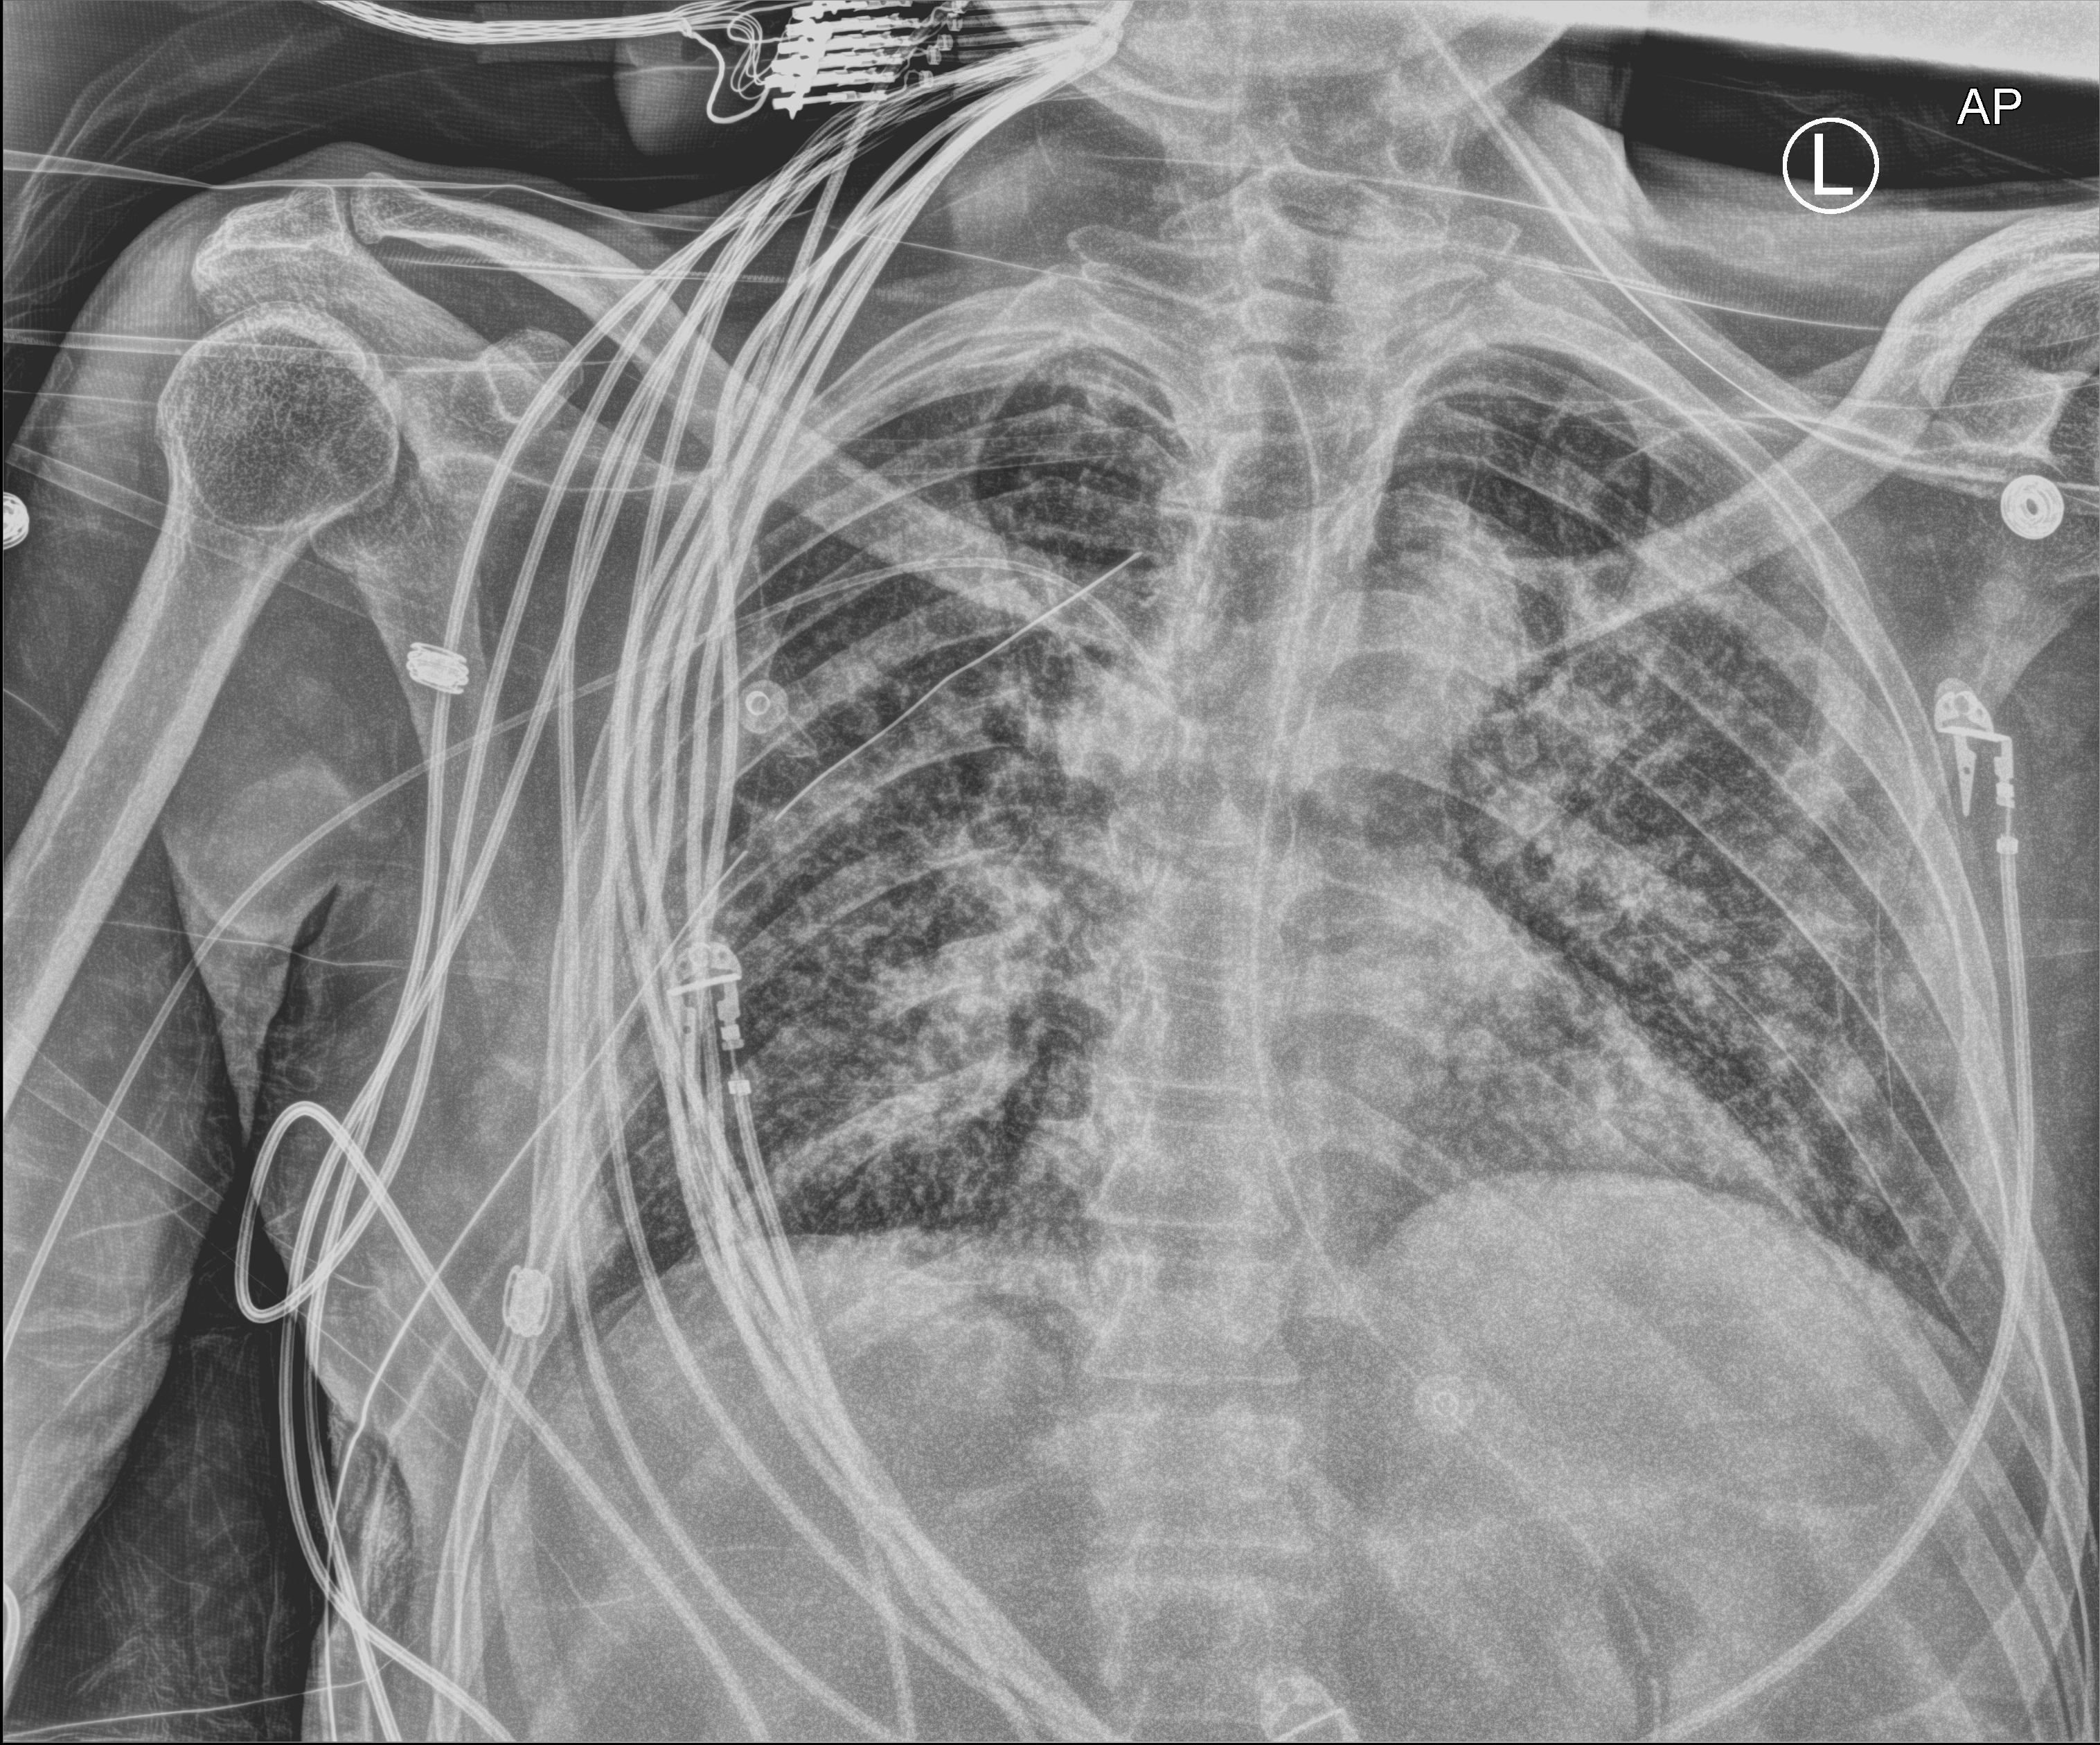
Bedside chest radiograph (computed radiography). Patient hospitalised with COVID-19; male, aged 18–59 years.
Hospital-stay facts (about this admission, not read from this image; timing relative to this image not recorded):
- hypertension (admission record): no
- admitted to intensive care during this hospital stay: yes